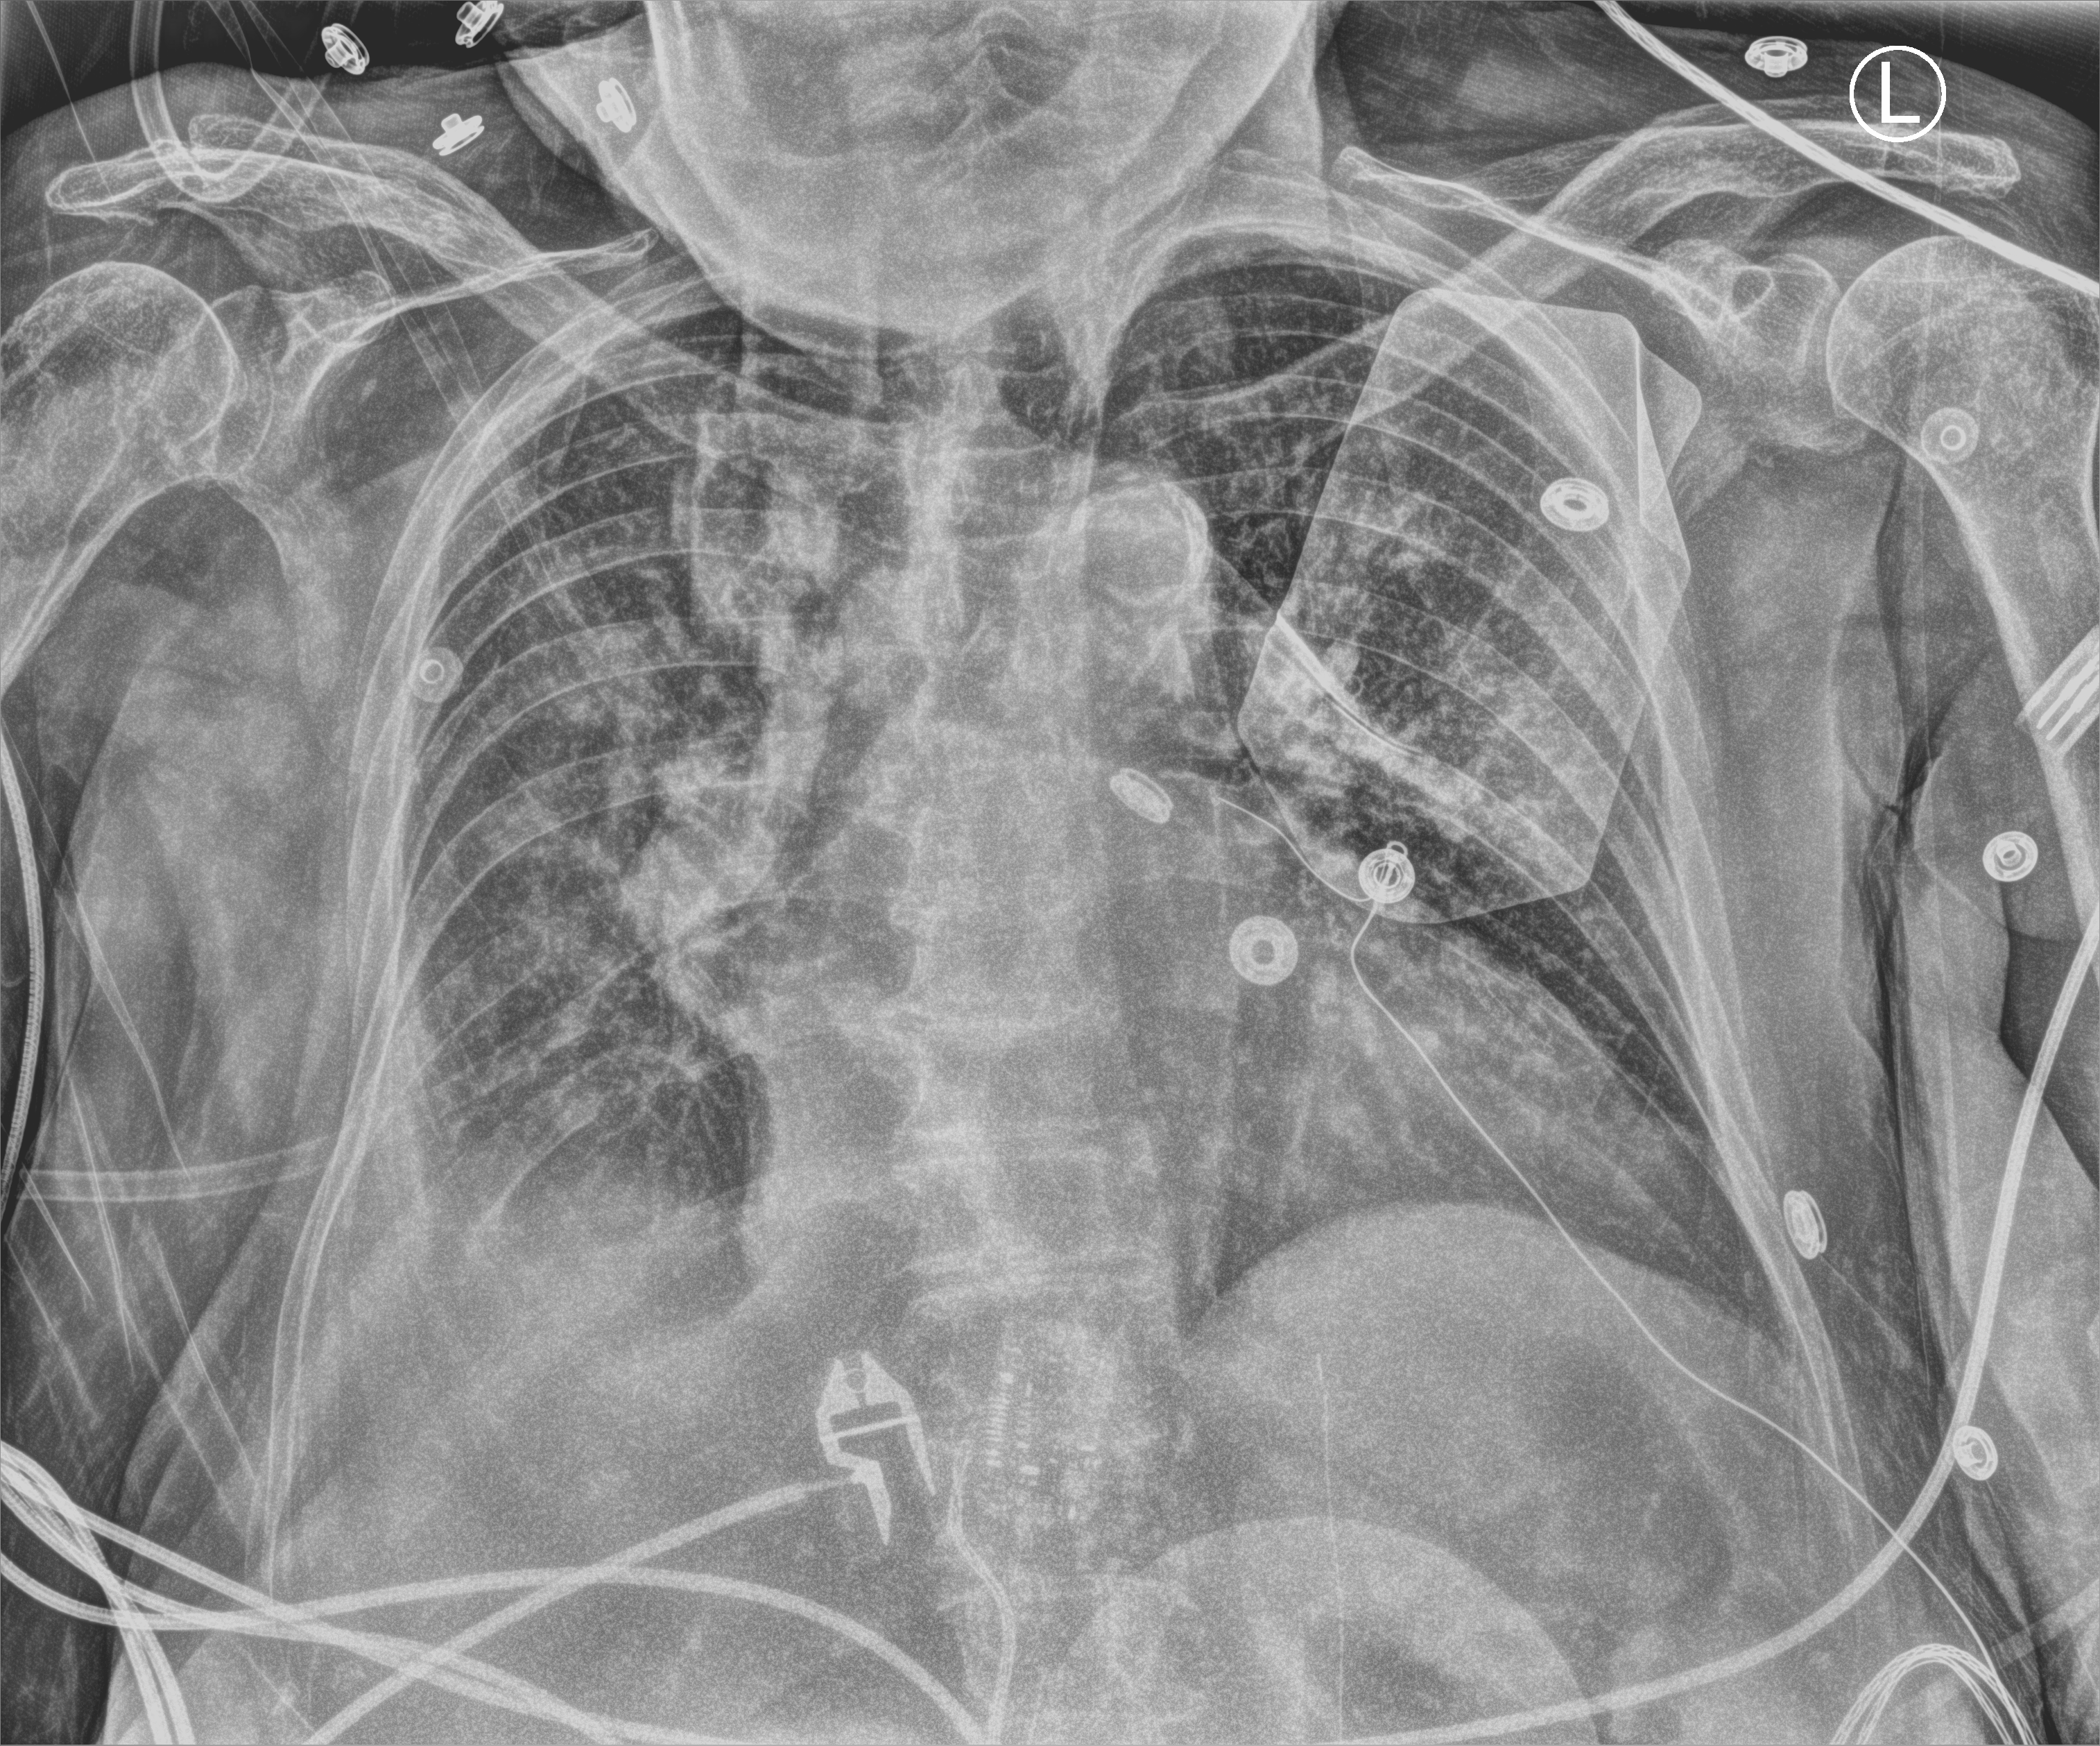
Bedside chest radiograph (computed radiography). Patient hospitalised with COVID-19; female, aged 75–90 years.
From the hospital-stay record, not from the radiograph (when in the stay this image was taken is not recorded): mechanically ventilated during this hospital stay: no; admitted to intensive care during this hospital stay: yes.